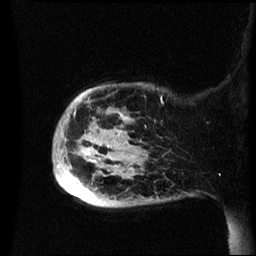
Breast MRI (dynamic contrast-enhanced), one sagittal slice; slice 8 of 60 in the series (ordered by position); dynamic contrast-enhanced series, image 2 of 3 at this slice position (ordered by acquisition); 1.5 T; TE 4.2 ms, TR 8.4 ms; 2.4 mm slice thickness; 256 × 256 image matrix, field of view 230 × 230 mm. Female patient, age 49 years.
Structures marked on this image (semi-automatically segmented with operator editing):
- analysis volume of interest (the breast-tissue region the enhancement analysis was run in; not a lesion): box from (x=53, y=83) to (x=174, y=207) px
- tumour enhancement mask (voxels above the 70 % enhancement threshold inside the analysis volume of interest): (x=78, y=114)–(x=123, y=200)